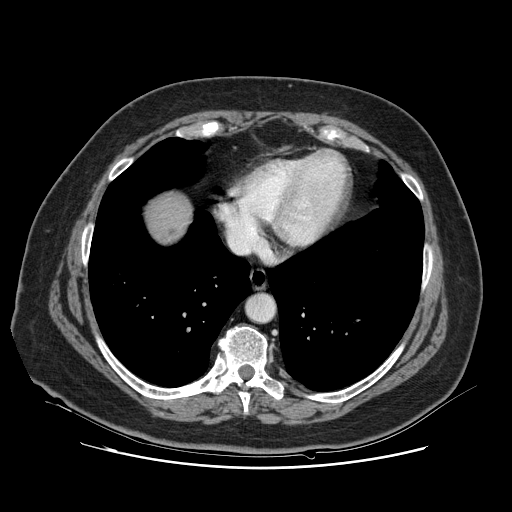
Contrast-enhanced abdominal CT, one axial slice; slice 121 of 132 in the series (ordered by position); intravenous contrast given; soft-tissue window (W 400 / L 40 HU); 2.5 mm slice thickness; 512 × 512 image matrix, field of view 391 × 391 mm. Female patient, age 73 years. From the clinical record (not read from this slice): diagnosis: colorectal cancer liver metastases, imaged before liver resection; multiple liver metastases: no; largest metastasis: 7 cm.
Annotated regions visible in this slice (expert manual segmentation):
- liver: bounding box (x1, y1, x2, y2) in pixels: (148, 197, 189, 241)
- planned liver remnant (the part of the liver to remain after resection): (149, 197, 189, 241)